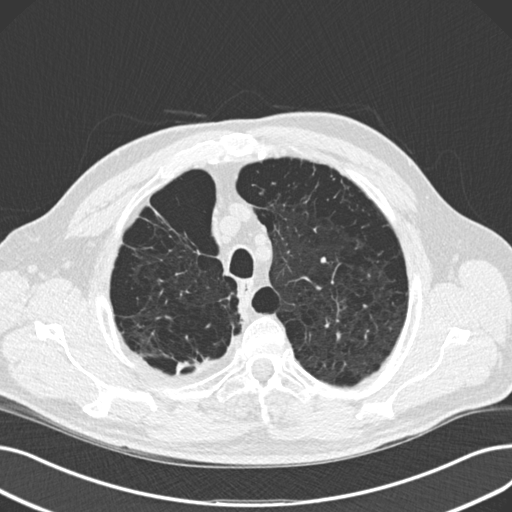
Low-dose screening chest CT, one axial slice. Slice 130 of 165 in the series (ordered by position). Lung window (W 1500 / L -600 HU). 2 mm slice thickness. 512 × 512 image matrix, field of view 369 × 369 mm.
Outlined on this slice (outlined manually by an expert reader):
- lesion 2 (tumor, upper lobe of right lung): bounding box [x1, y1, x2, y2] px = [177, 362, 189, 372]